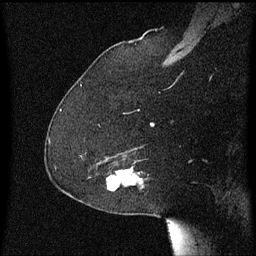
Breast MRI (dynamic contrast-enhanced), one sagittal slice; dynamic contrast-enhanced series, image 2 of 3 at this slice position (ordered by acquisition); 1.5 T; TE 4.2 ms, TR 8.4 ms; 2 mm slice thickness; 256 × 256 image matrix, field of view 200 × 200 mm. Female patient, age 59 years.
Annotated regions visible in this slice (semi-automatically segmented with operator editing):
- analysis volume of interest (the breast-tissue region the enhancement analysis was run in; not a lesion): box from (x=90, y=168) to (x=149, y=191) px
- tumour enhancement mask (voxels above the 70 % enhancement threshold inside the analysis volume of interest): (x=132, y=178)–(x=143, y=185)